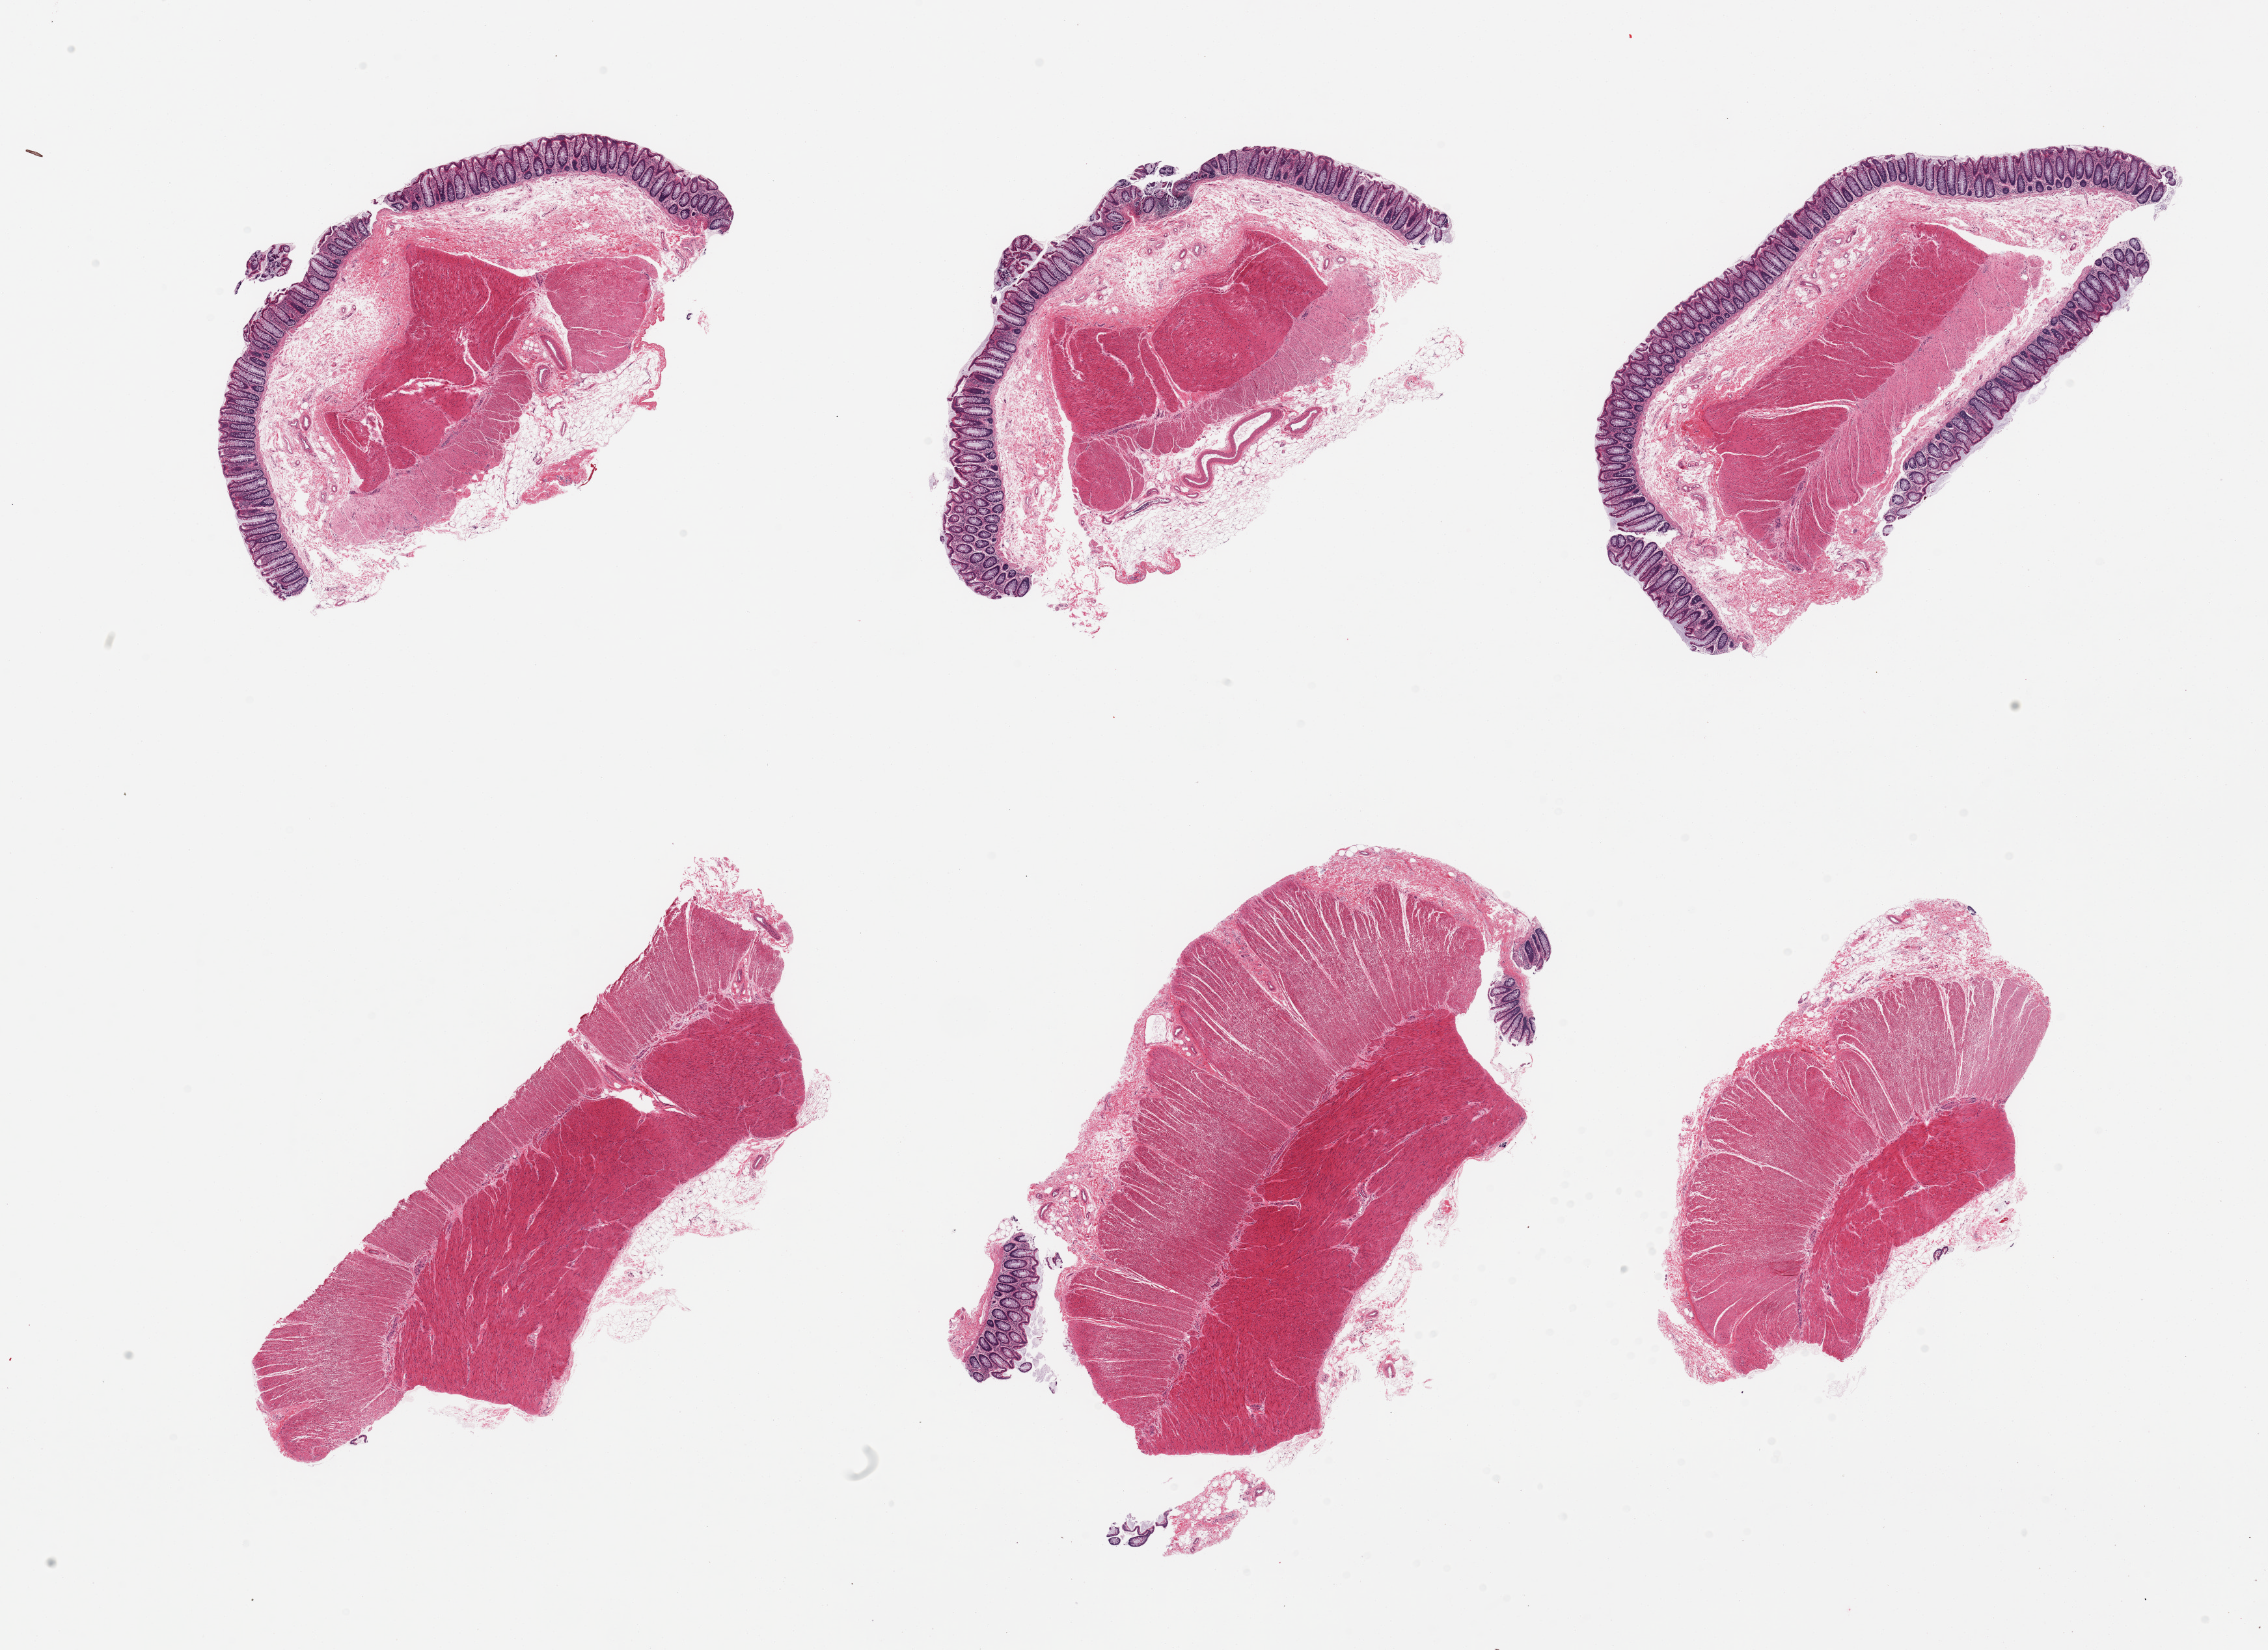
Hematoxylin and eosin (H&E) whole-slide image, brightfield, shown as a low-resolution overview of the whole scanned area (about 27.6 x 20.1 mm, from a 20x scan). Donor sex: male.
Specimen: PAXgene-fixed paraffin-embedded (PFPE) section; section of sigmoid colon (target tissue); tissue donor sample.